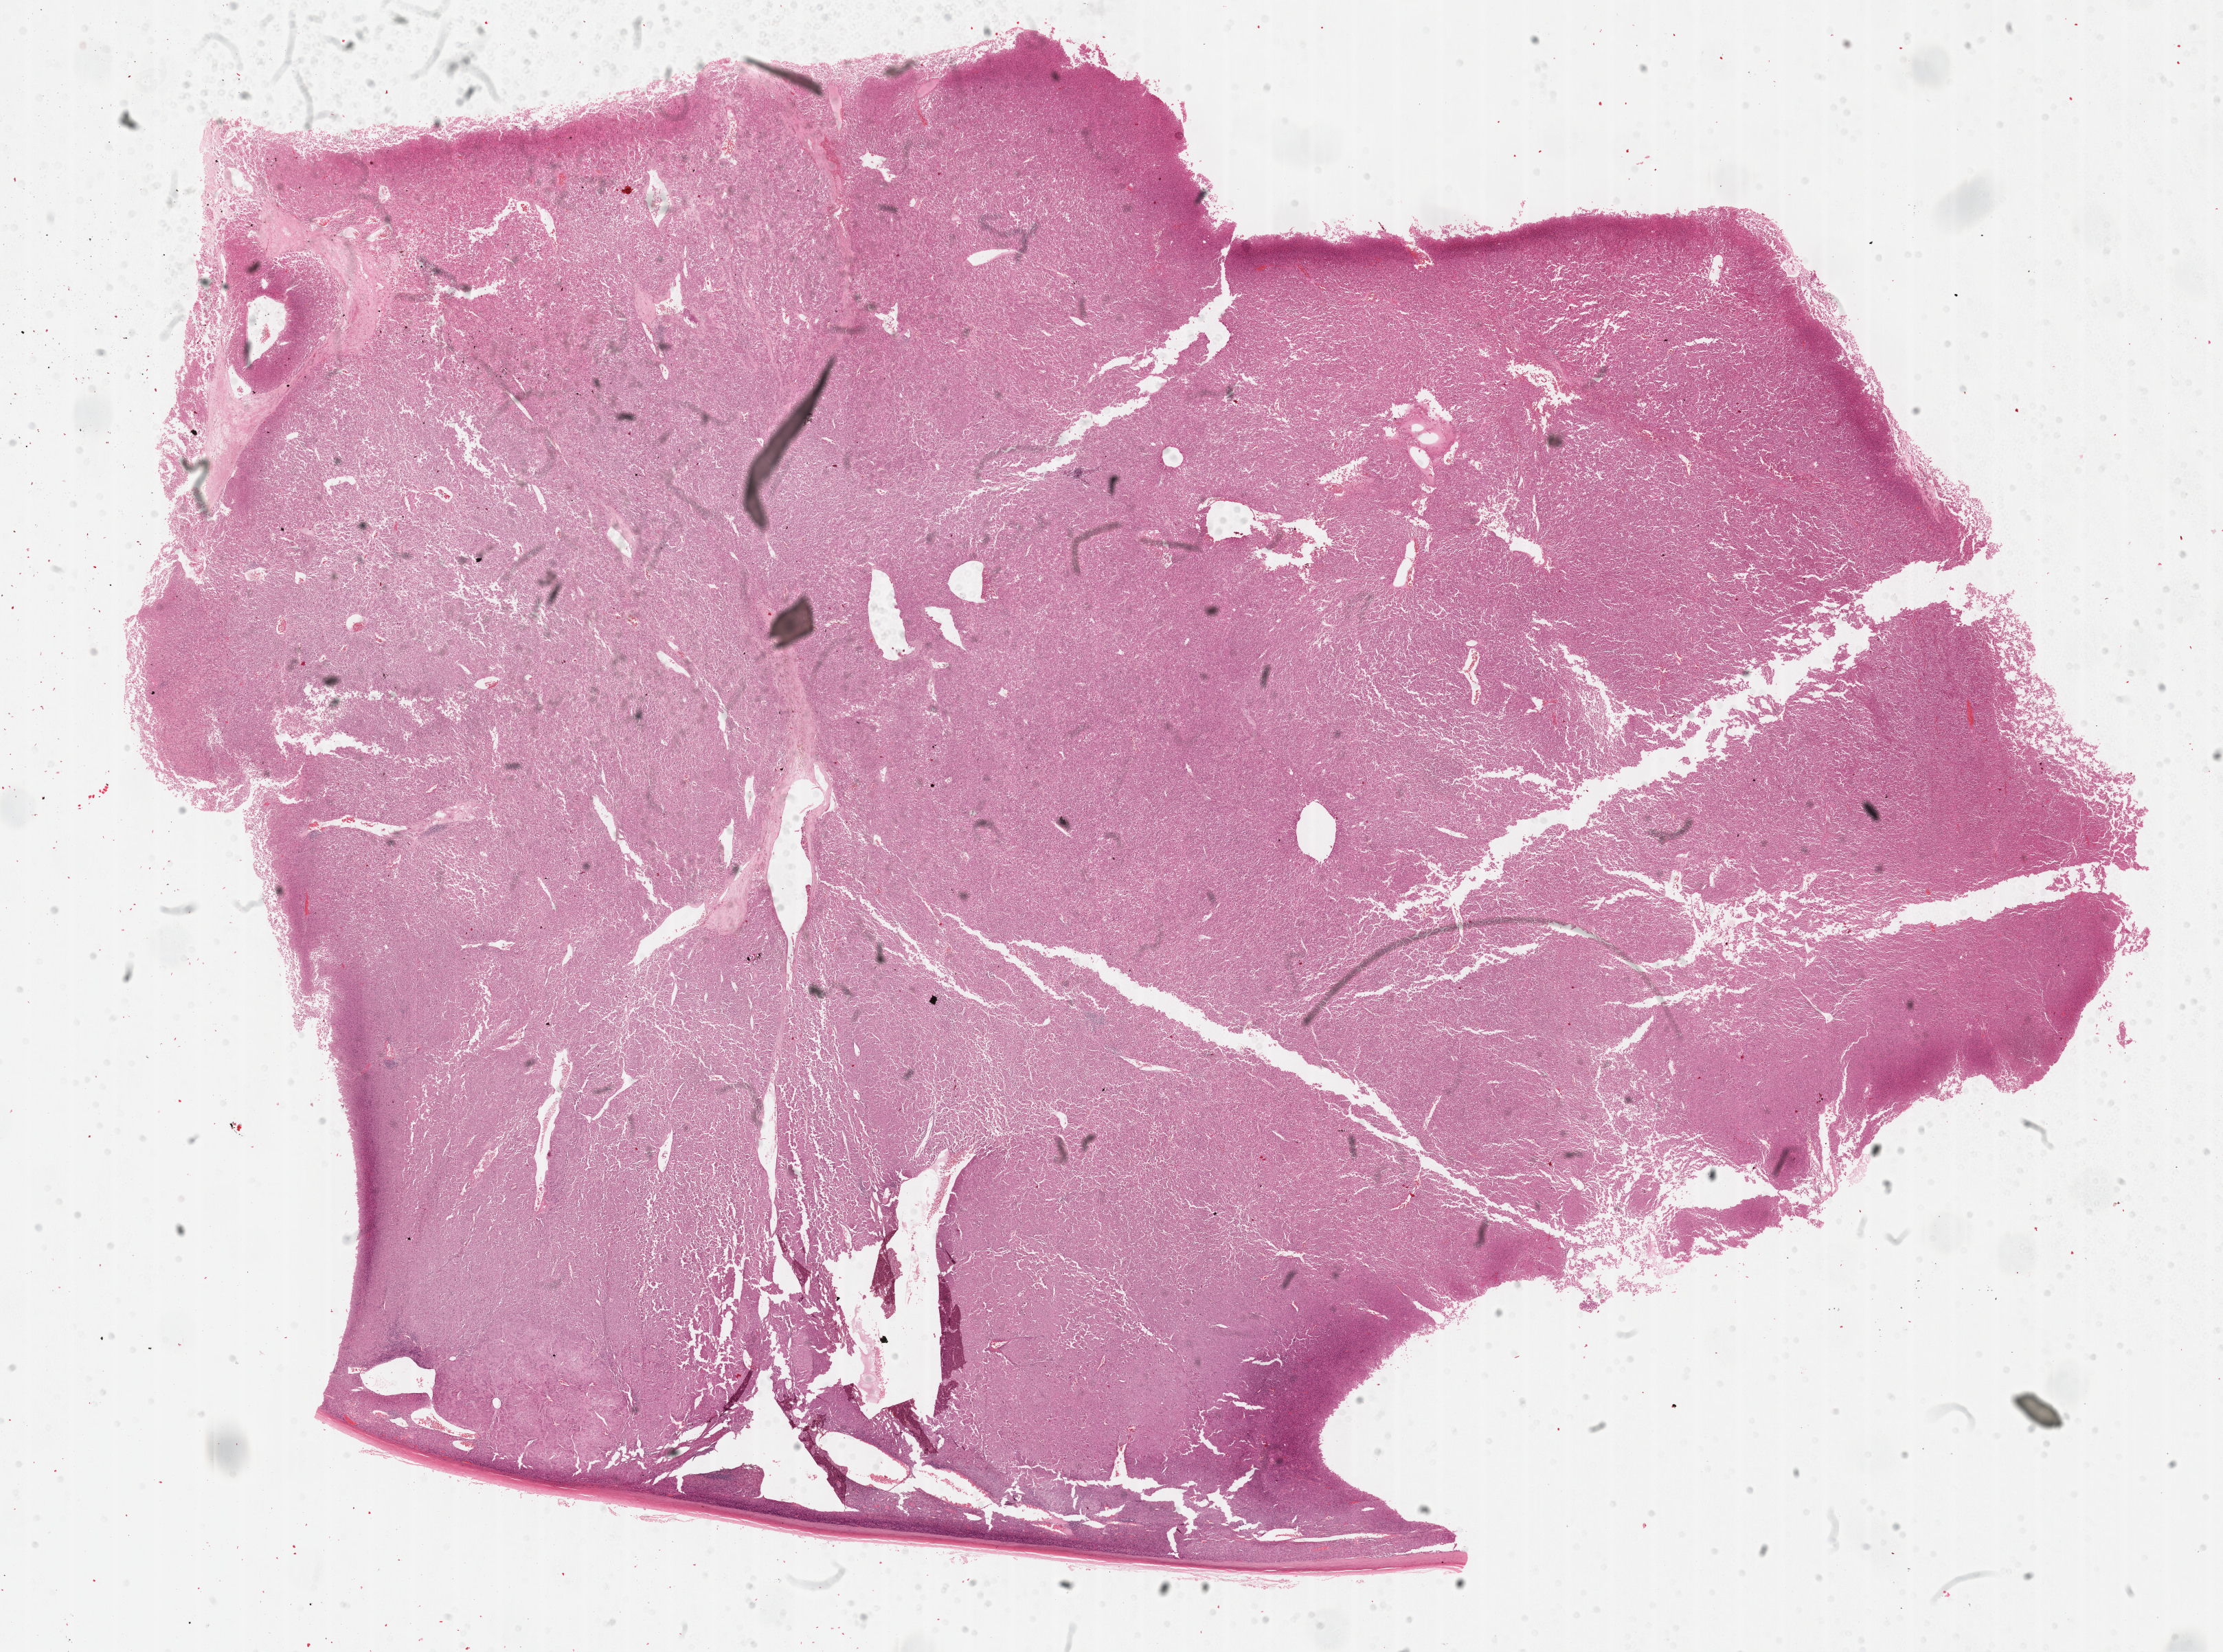
Digitized H&E-stained tissue section (whole slide), low-resolution overview of the scanned area, about 26.2 x 19.5 mm (slide scanned at 40x). Formalin-fixed paraffin-embedded (FFPE) diagnostic section. Primary tumour sample from the adrenal cortex. Male, age 49 years at initial diagnosis.
* histologic diagnosis: Adrenal cortical carcinoma (cortex of adrenal gland)